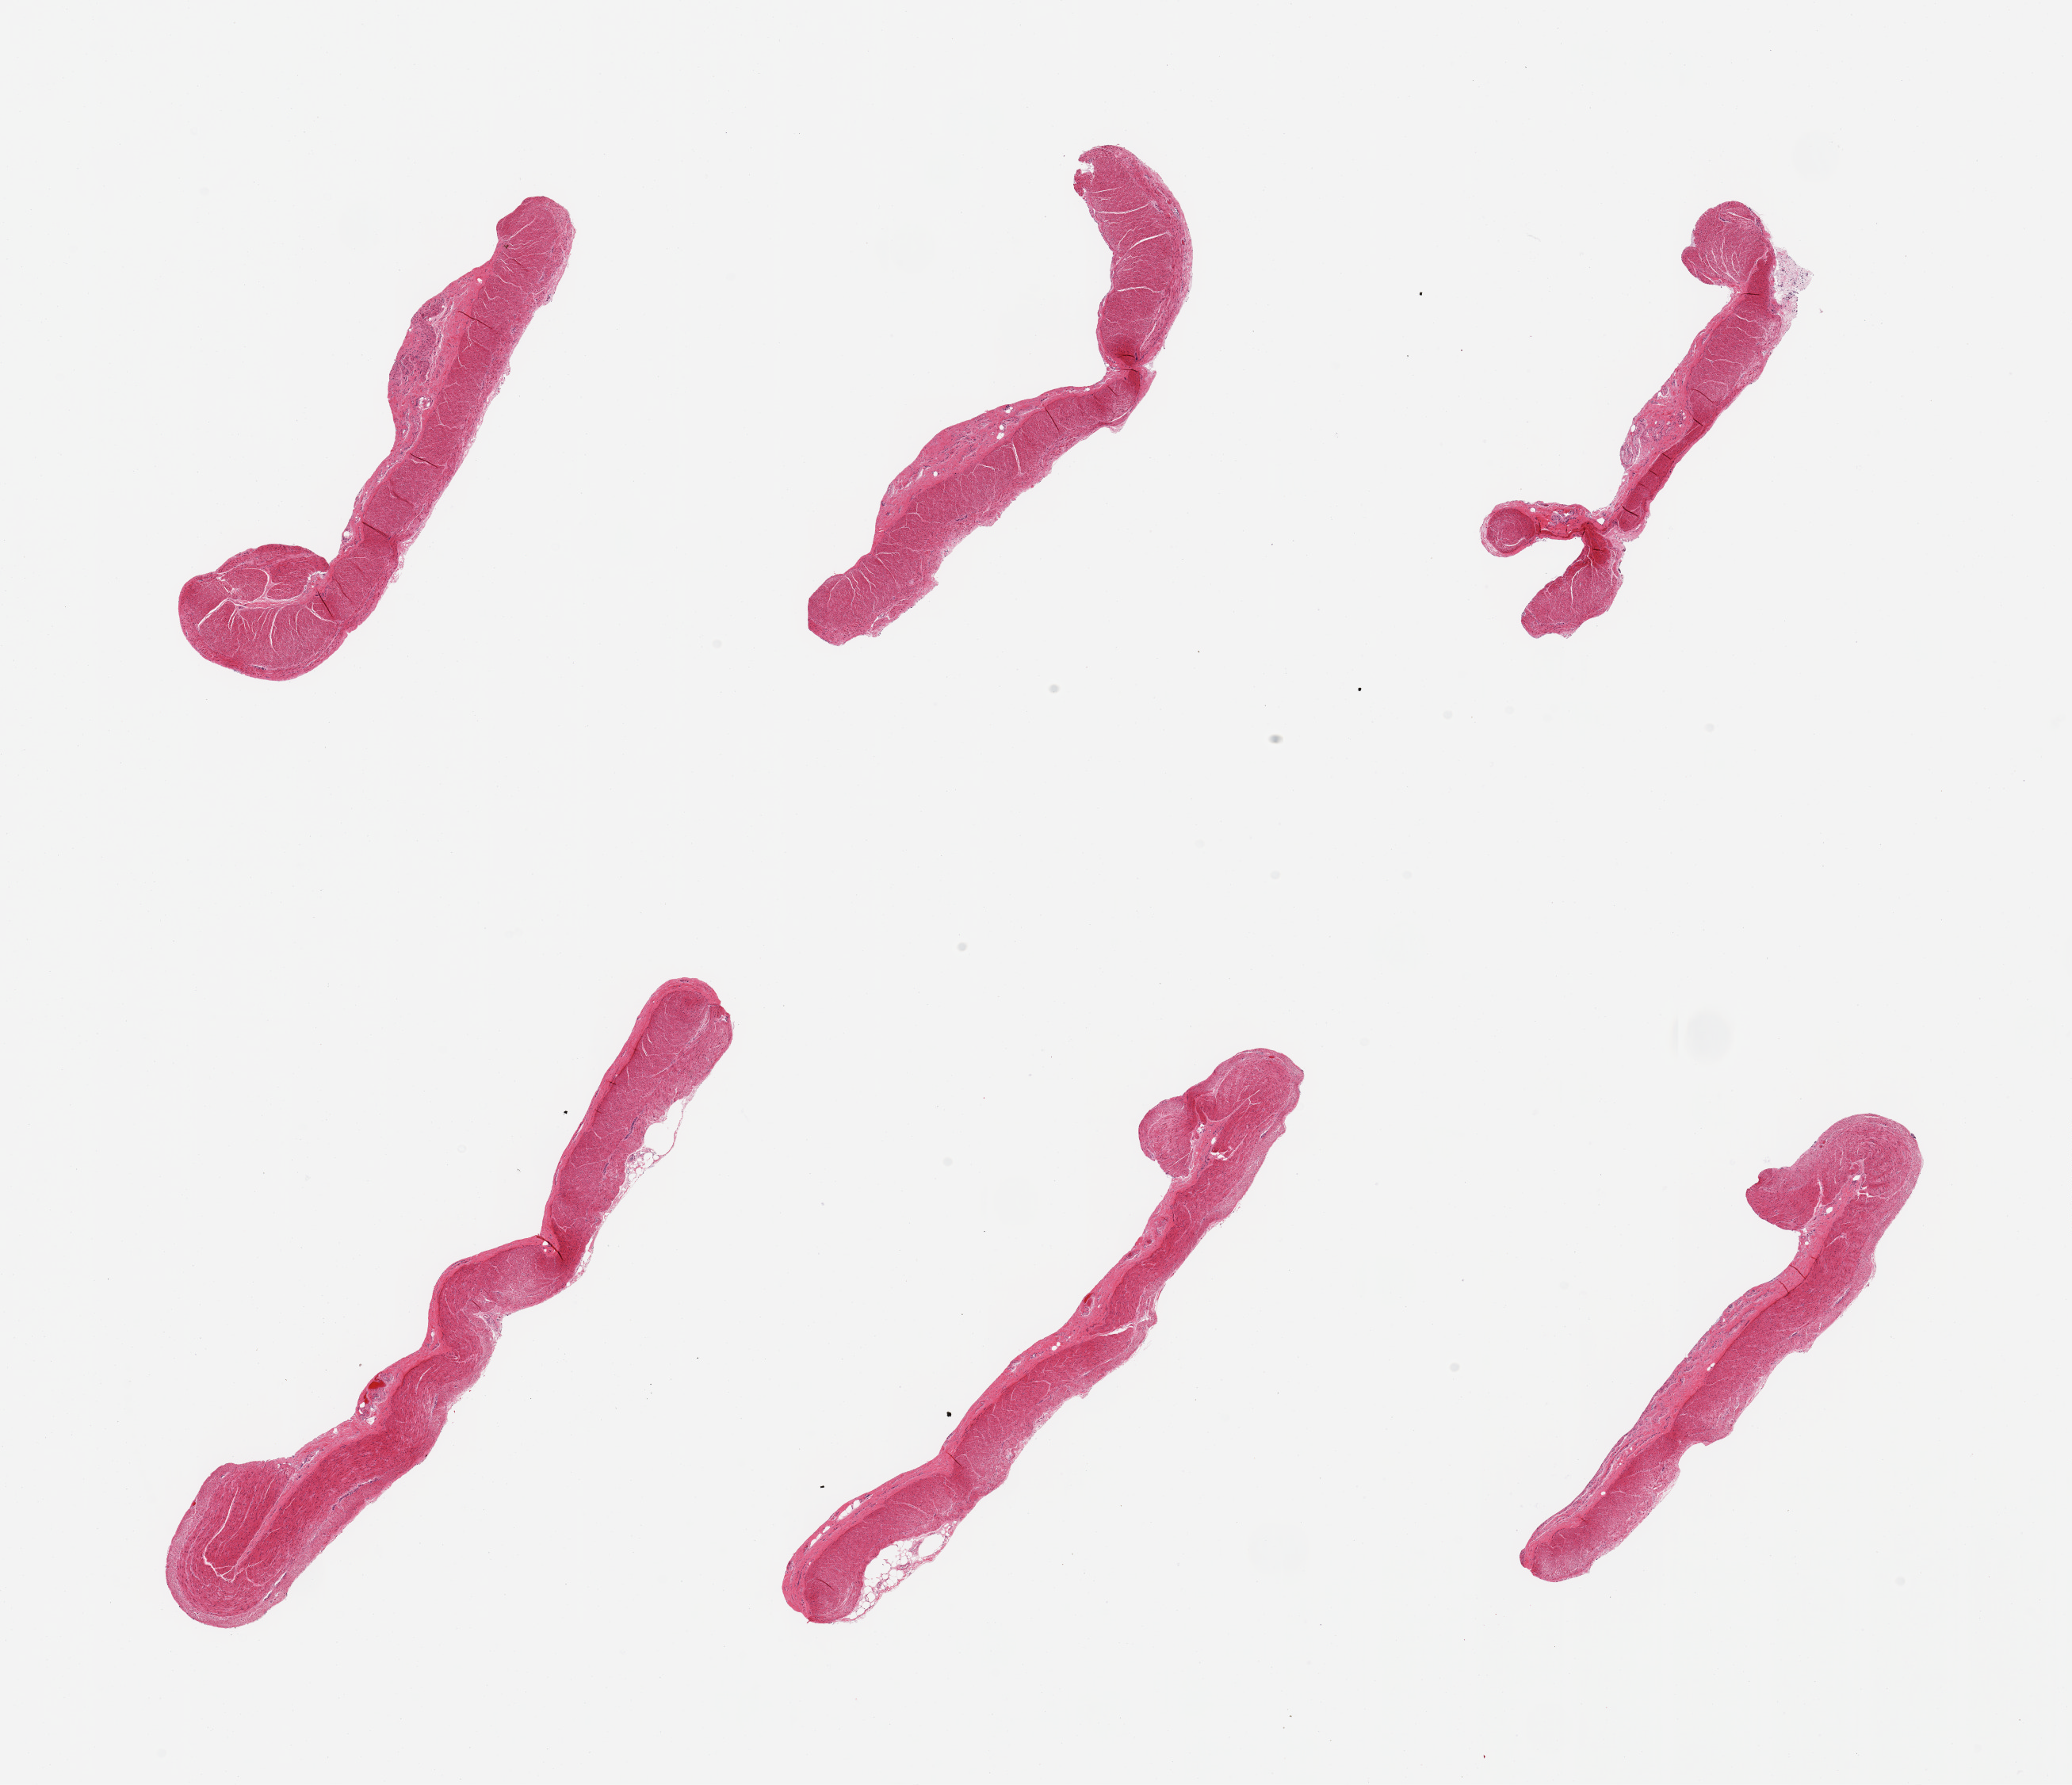
Hematoxylin and eosin (H&E) whole-slide image, brightfield, low-resolution overview of the scanned area, about 20.7 x 17.8 mm (acquisition: 20x scan). PAXgene-fixed, paraffin-embedded tissue. Target tissue: sigmoid colon. Tissue donor sample. Donor: female.
* pathologist's review note for this sample: 6 pieces; foci of fibrovascular stroma occupy up to 10%